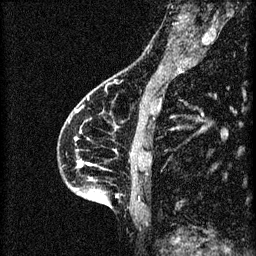
Breast MRI (dynamic contrast-enhanced), one sagittal slice; slice 24 of 60 in the series (ordered by position); 3 images stored at this slice position (order not interpretable as contrast timing); 1.5 T; TE 4.2 ms, TR 8.2 ms; 2 mm slice thickness; 256 × 256 image matrix, field of view 180 × 180 mm. Female patient, age 46 years.
Structures marked on this image (semi-automatically segmented with operator editing):
- analysis volume of interest (the breast-tissue region the enhancement analysis was run in; not a lesion): bounding box [x1, y1, x2, y2] px = [58, 114, 148, 209]
- tumour enhancement mask (voxels above the 70 % enhancement threshold inside the analysis volume of interest): [76, 162, 91, 191]